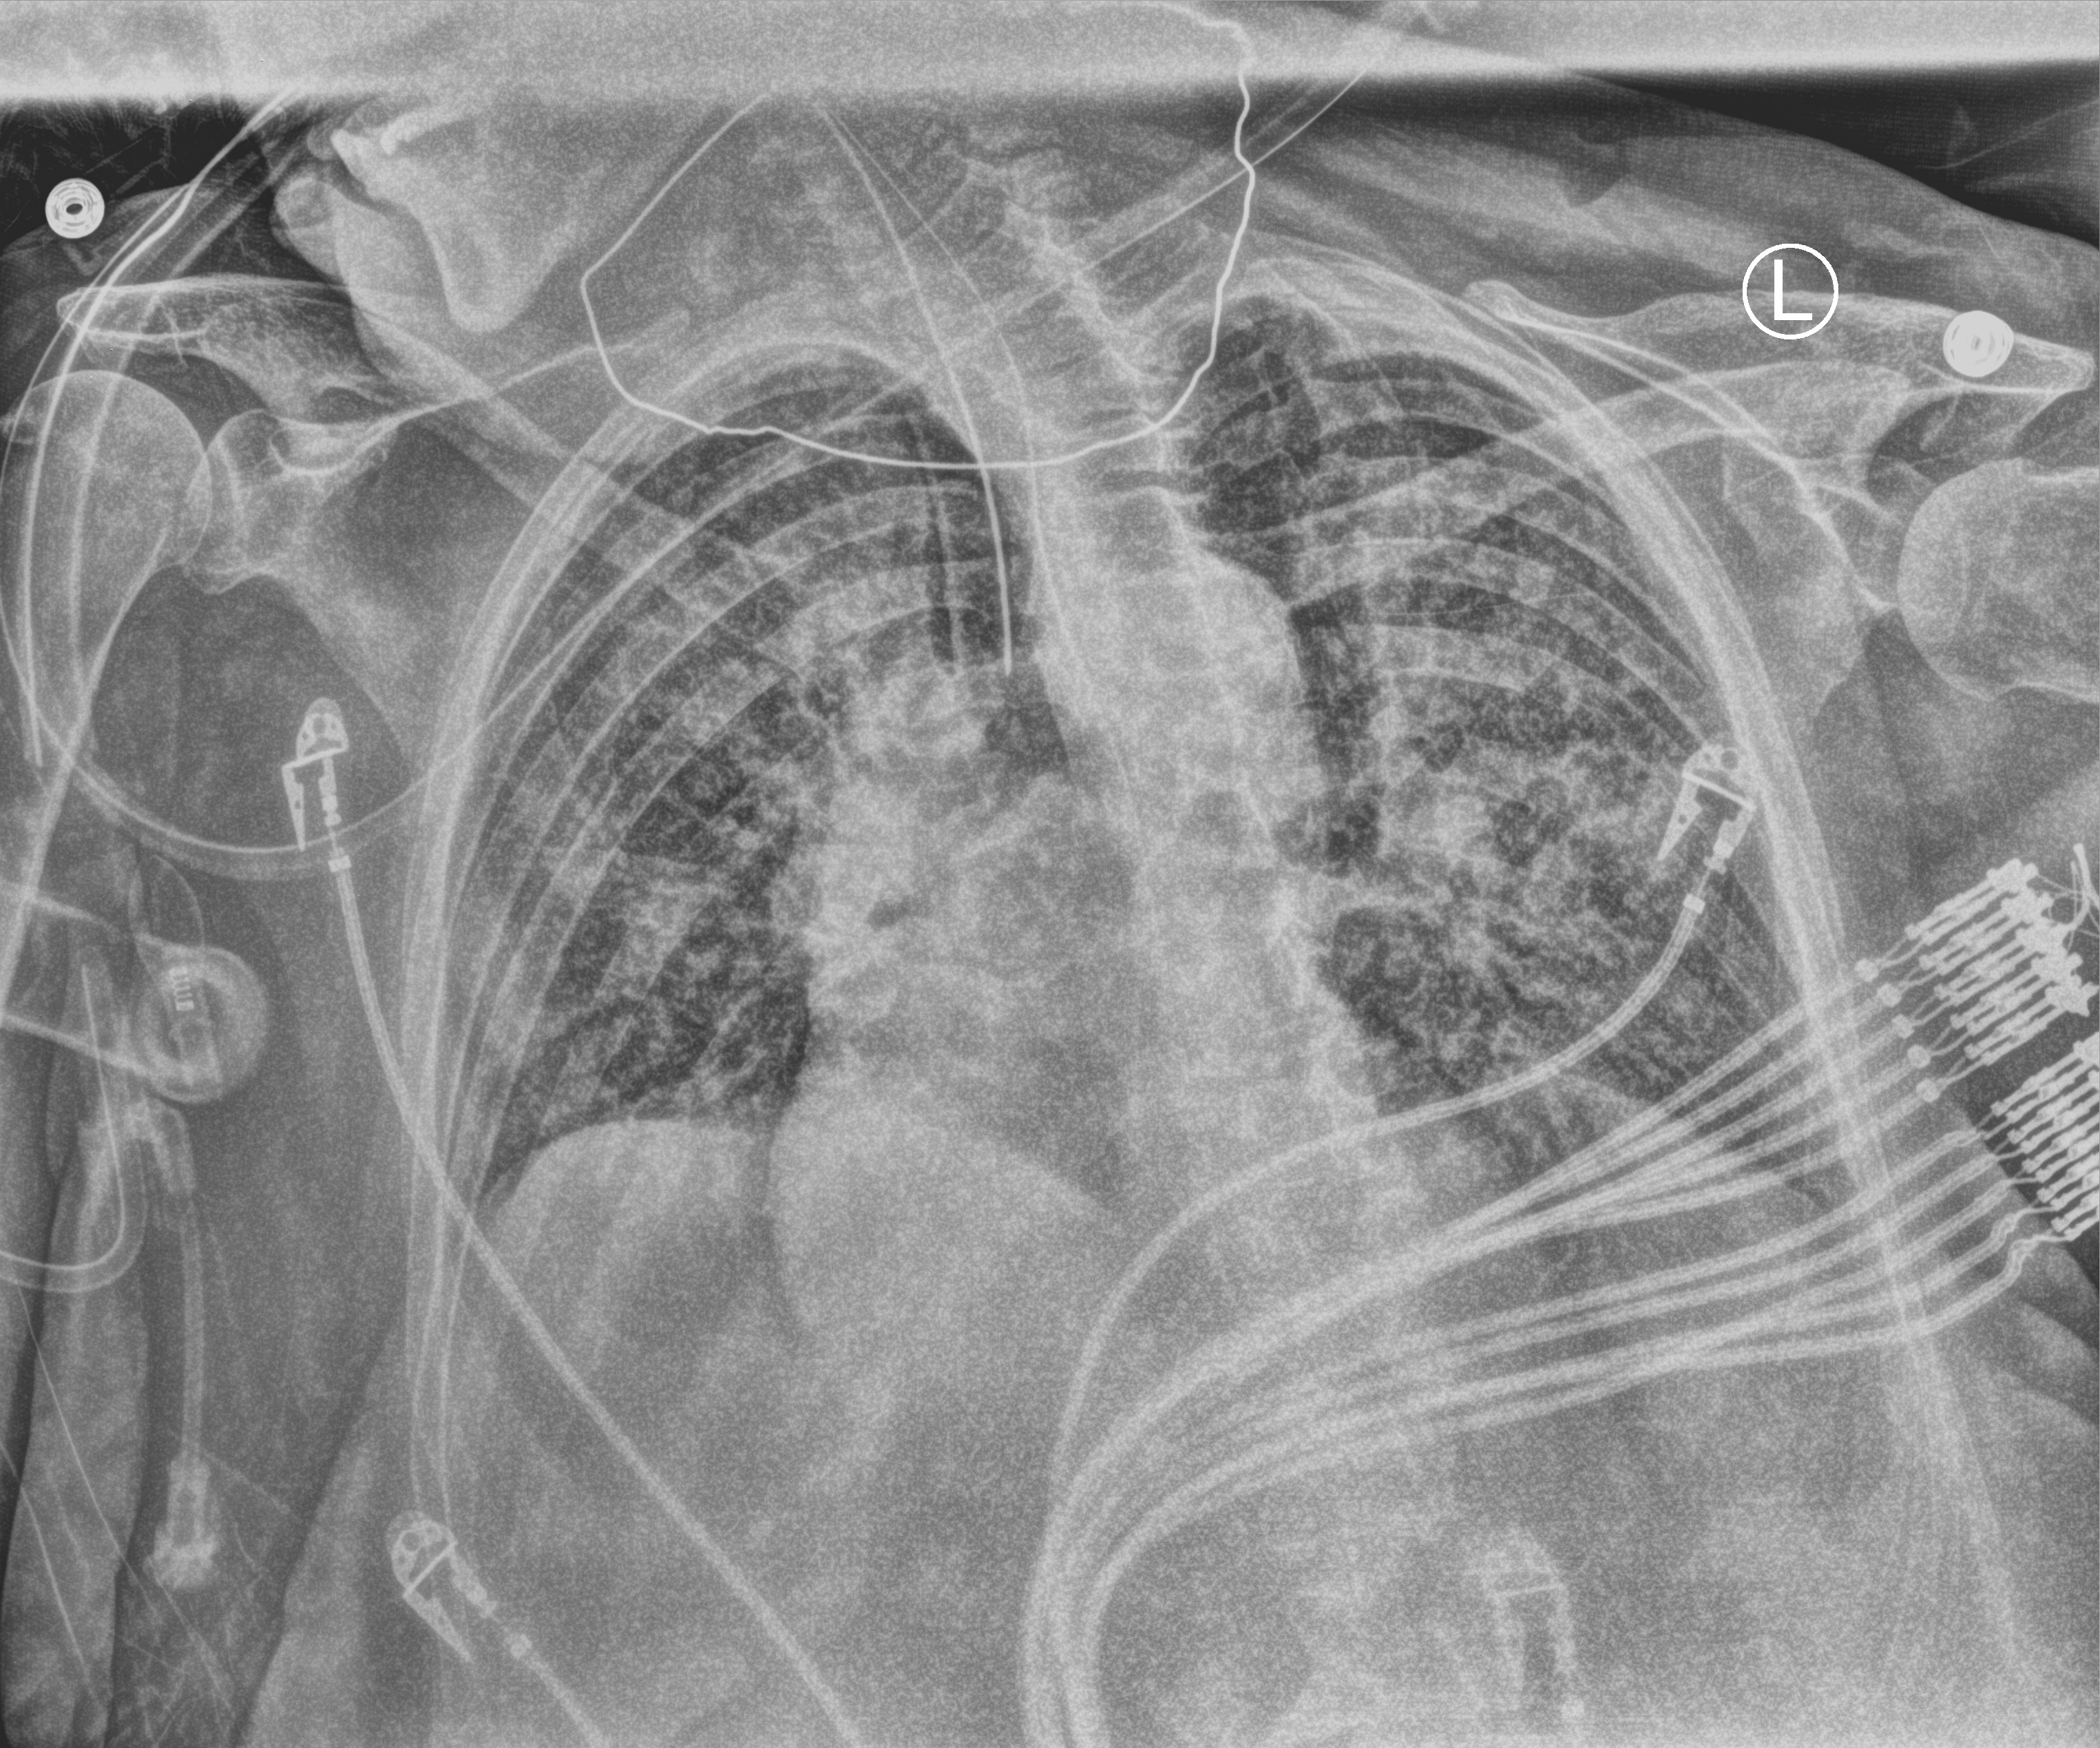
Bedside chest radiograph (computed radiography), anteroposterior (AP) projection. Patient hospitalised with COVID-19; female, aged 75–90 years.
Hospital-stay facts (about this admission, not read from this image; timing relative to this image not recorded): admitted to intensive care during this hospital stay: yes.